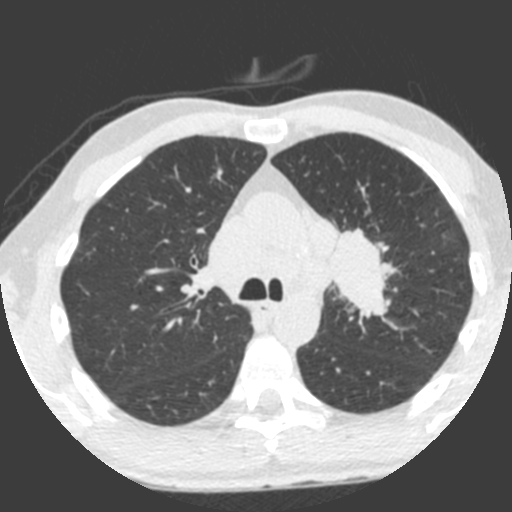
Low-dose screening chest CT, axial slice; third annual screen; lung window (W 1500 / L -600 HU); 2 mm slice thickness; standard (soft-tissue) reconstruction kernel (B); 120 kVp. Male participant, aged 55 years at enrolment.
- Expert reader's lesion annotation, bounding box <309,228,392,323> (left, top, right, bottom; pixels).
- The exam's reader record, not a measurement of the box and not confirmed to be the same lesion: non-calcified nodule or mass ≥4 mm, left upper lobe, 49 × 29 mm, spiculated (stellate) margins, soft tissue attenuation, pre-existing on the prior screen: yes; interval growth: yes.
- Lung cancer was diagnosed 0 days after this screen: small cell carcinoma, NOS, left upper lobe, undifferentiated (G4), stage IV (AJCC 6th edition), 60 mm at pathology.